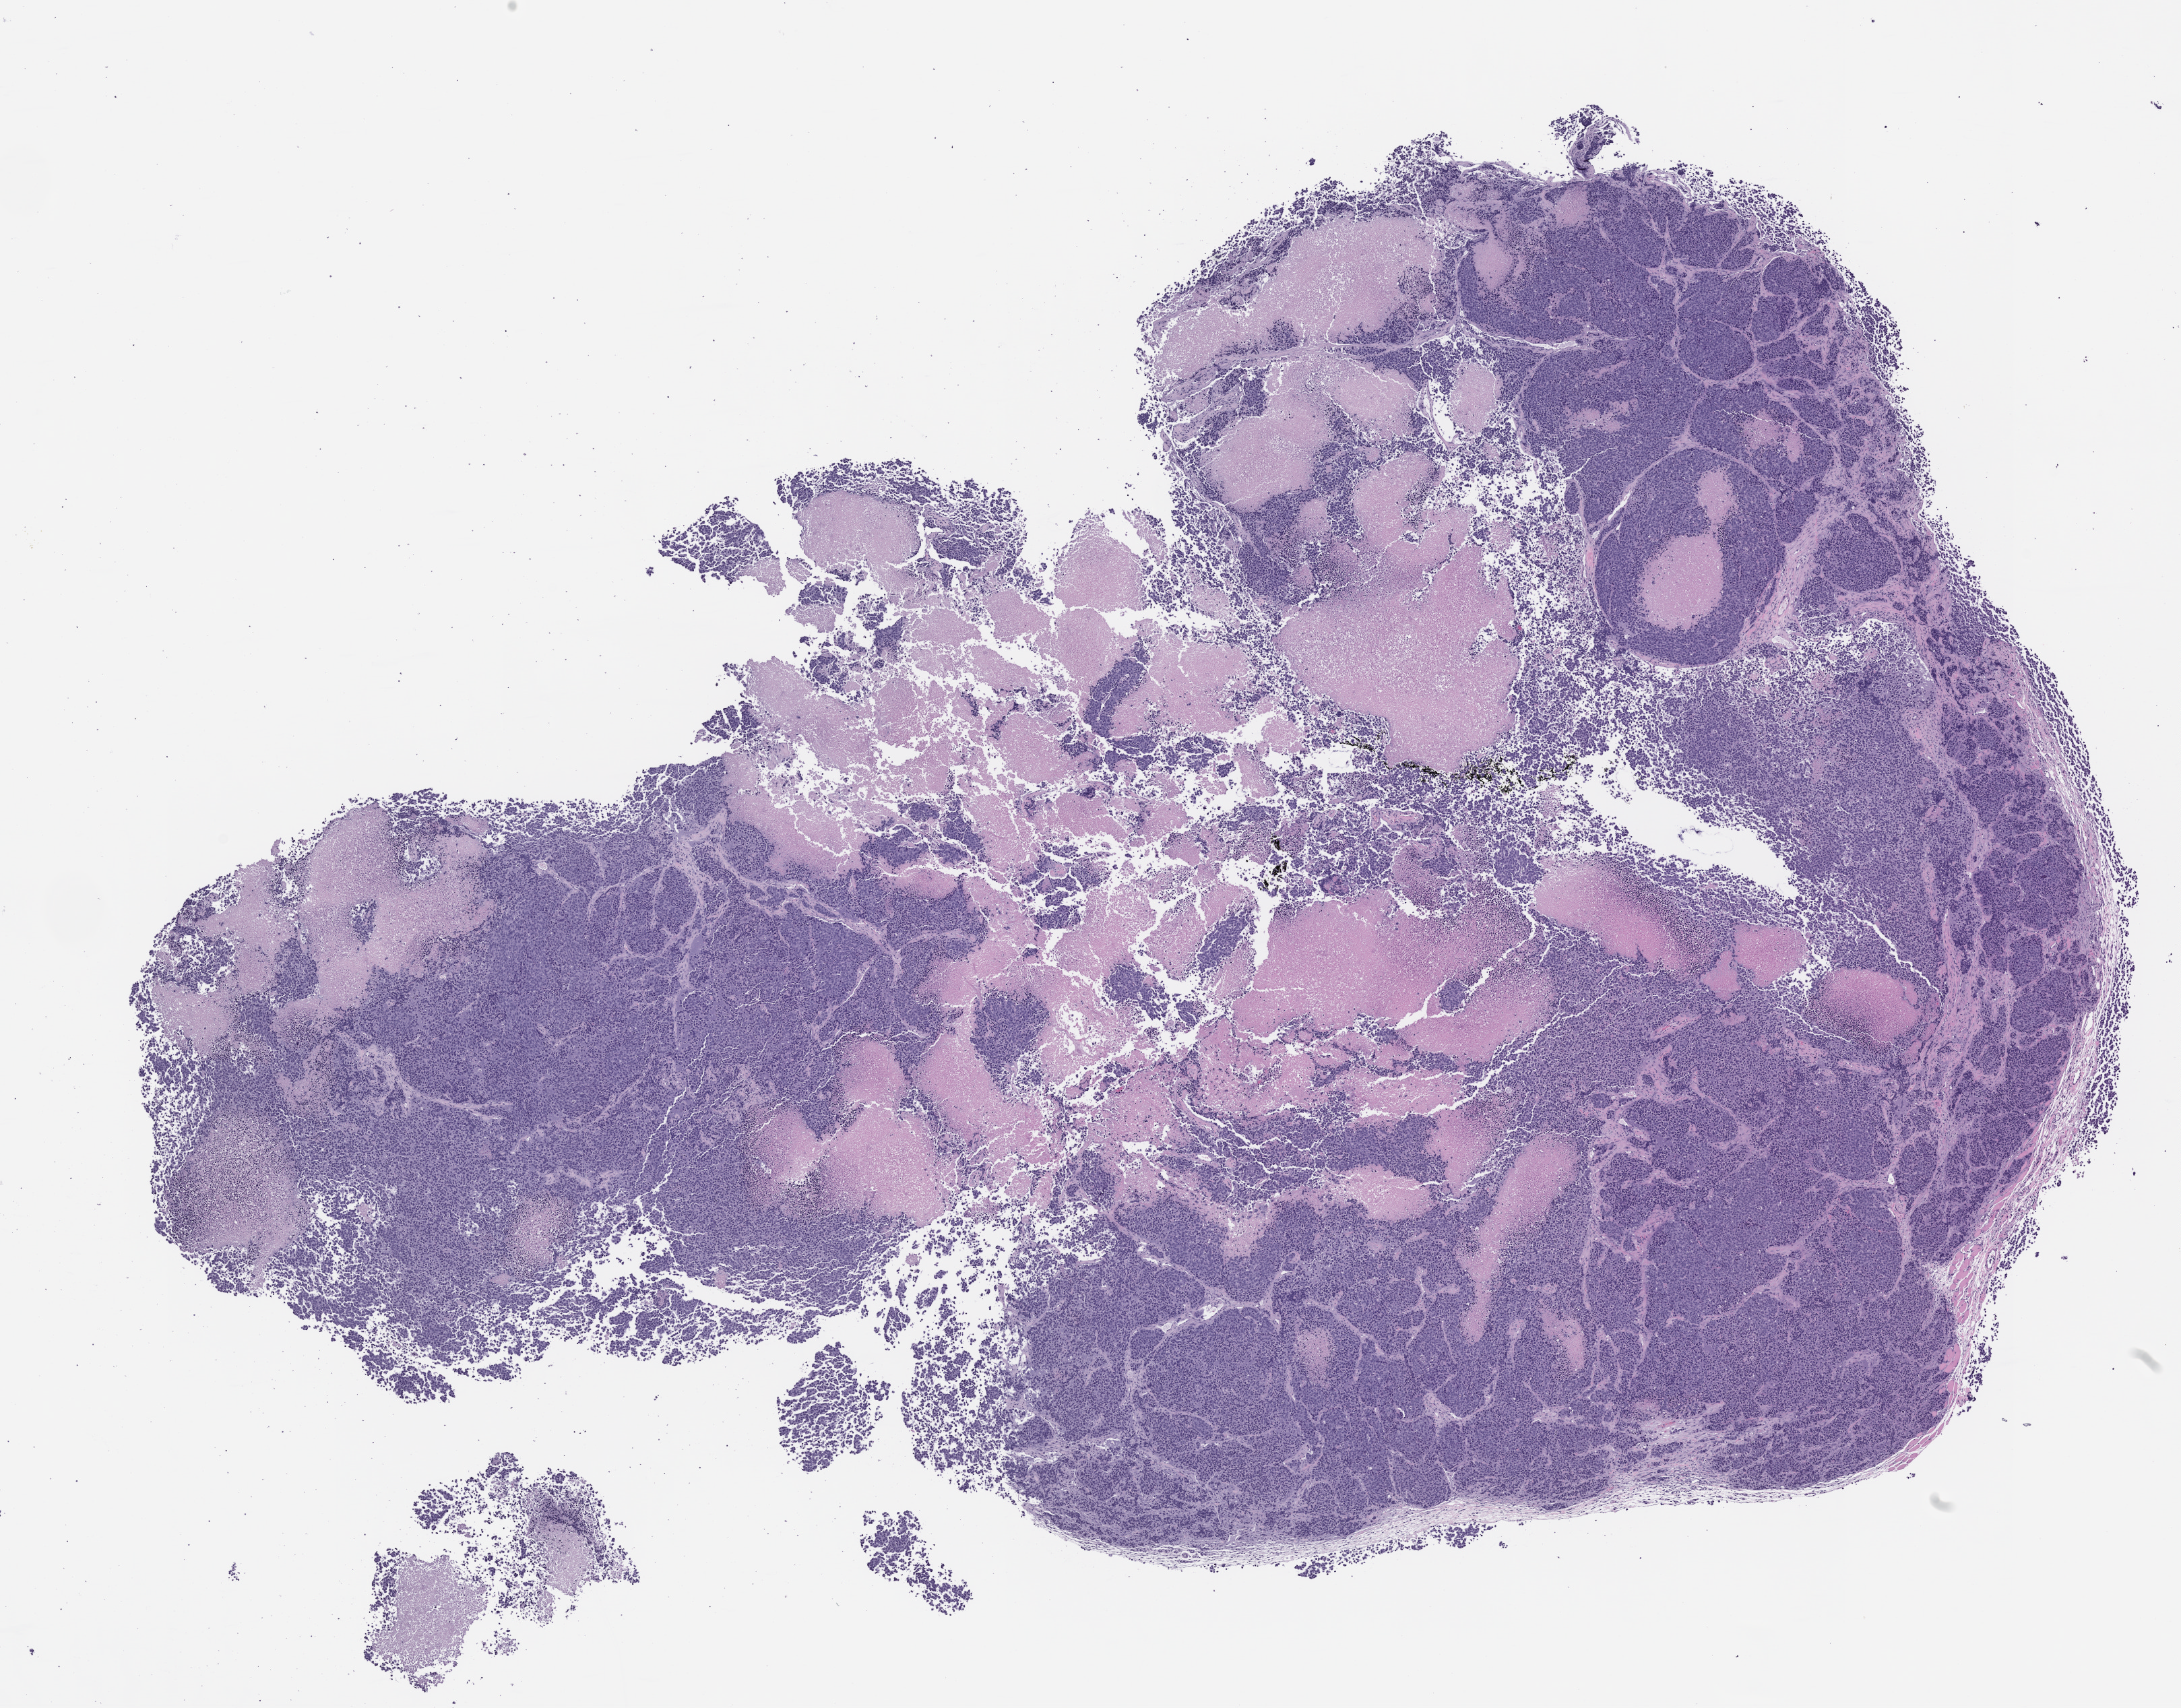
Whole-slide image, H&E: patient-derived xenograft (human tumor grown in a mouse), passage 0 — whole scanned area (about 13.0 x 10.2 mm) shown as a low-resolution overview; FFPE section; originating tumor site category: neuroendocrine system.
Originating patient diagnosis: Neuroendocrine Carcinoma.